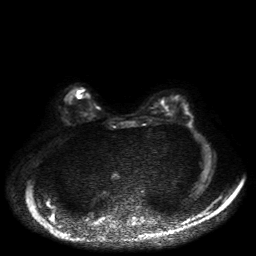
Breast MRI, one axial slice. Position 18 of 50 along the scan axis. Diffusion-weighted series; image 2 of 4 stored at this slice position (different b-values; order by instance number). 1.5 T. 256 × 256 image matrix. Female patient.
Structures marked on this image (expert manual segmentation):
- tumour on diffusion-weighted imaging: bounding box [x1, y1, x2, y2] px = [77, 95, 80, 97]